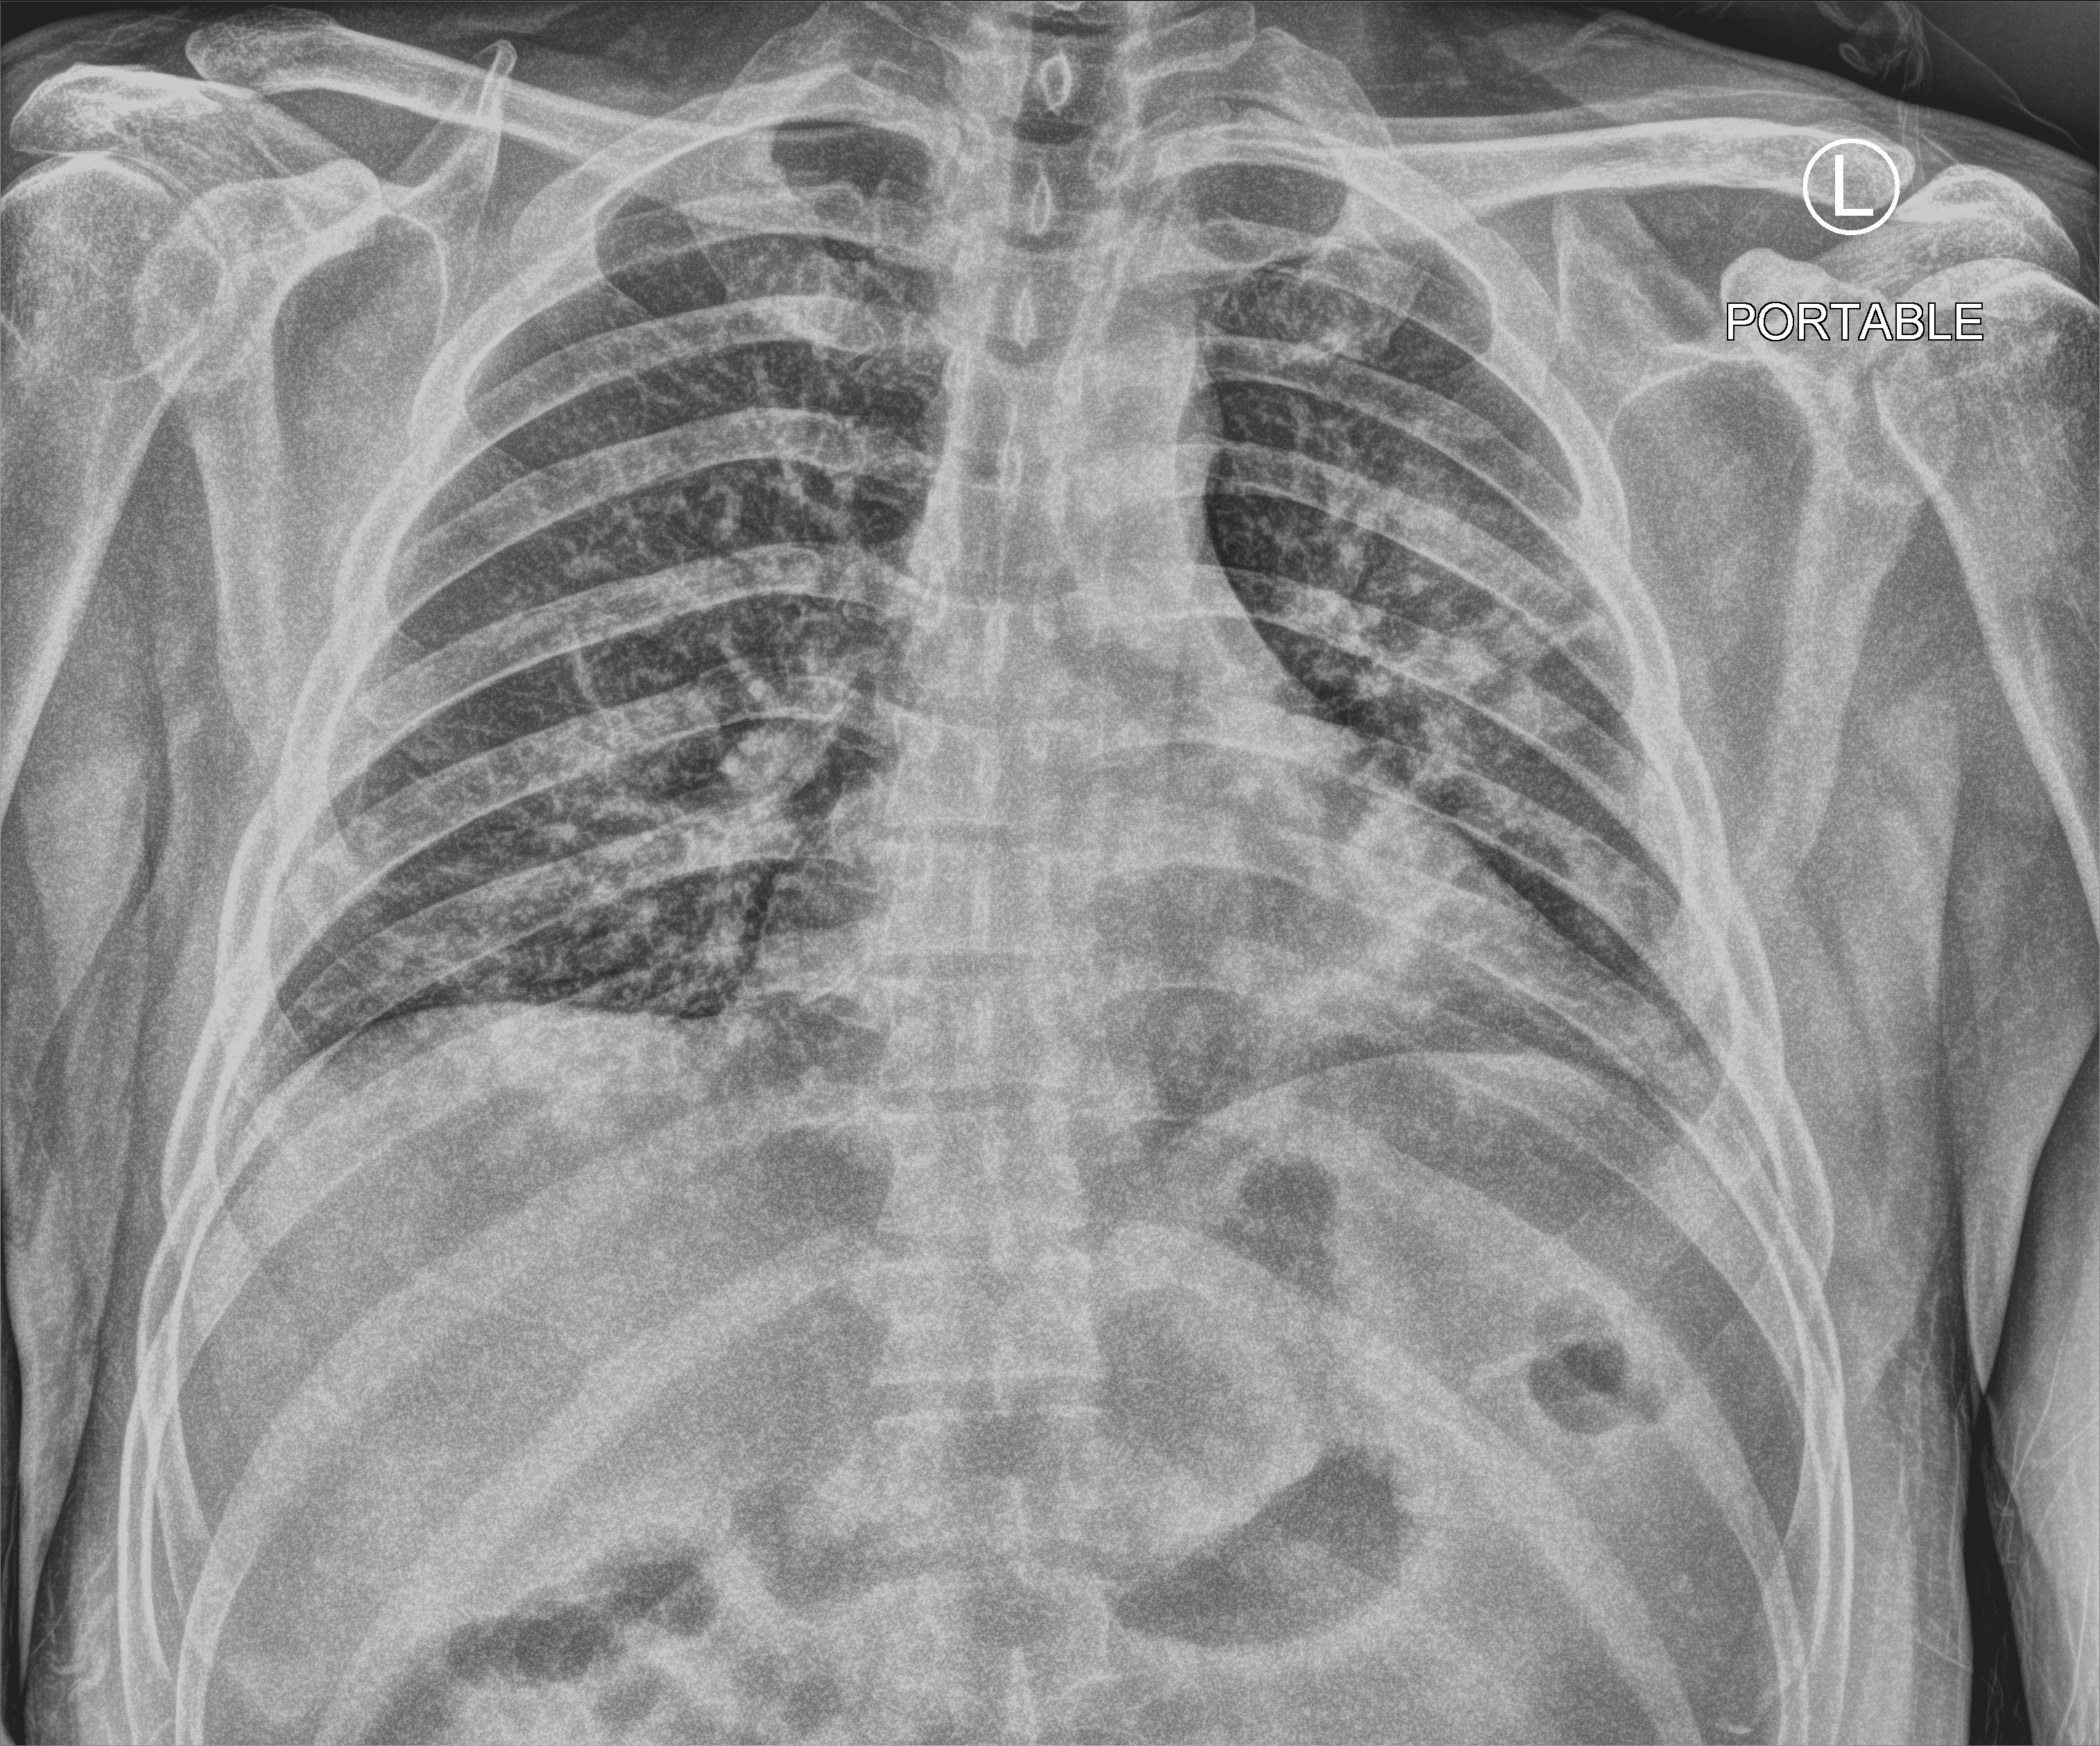
Chest X-ray (portable); anteroposterior (AP) projection. Male patient hospitalised with COVID-19, age 18–59 years.
Admission-level facts for this patient (not findings on this image; timing relative to this image not recorded):
- mechanically ventilated during this hospital stay: no